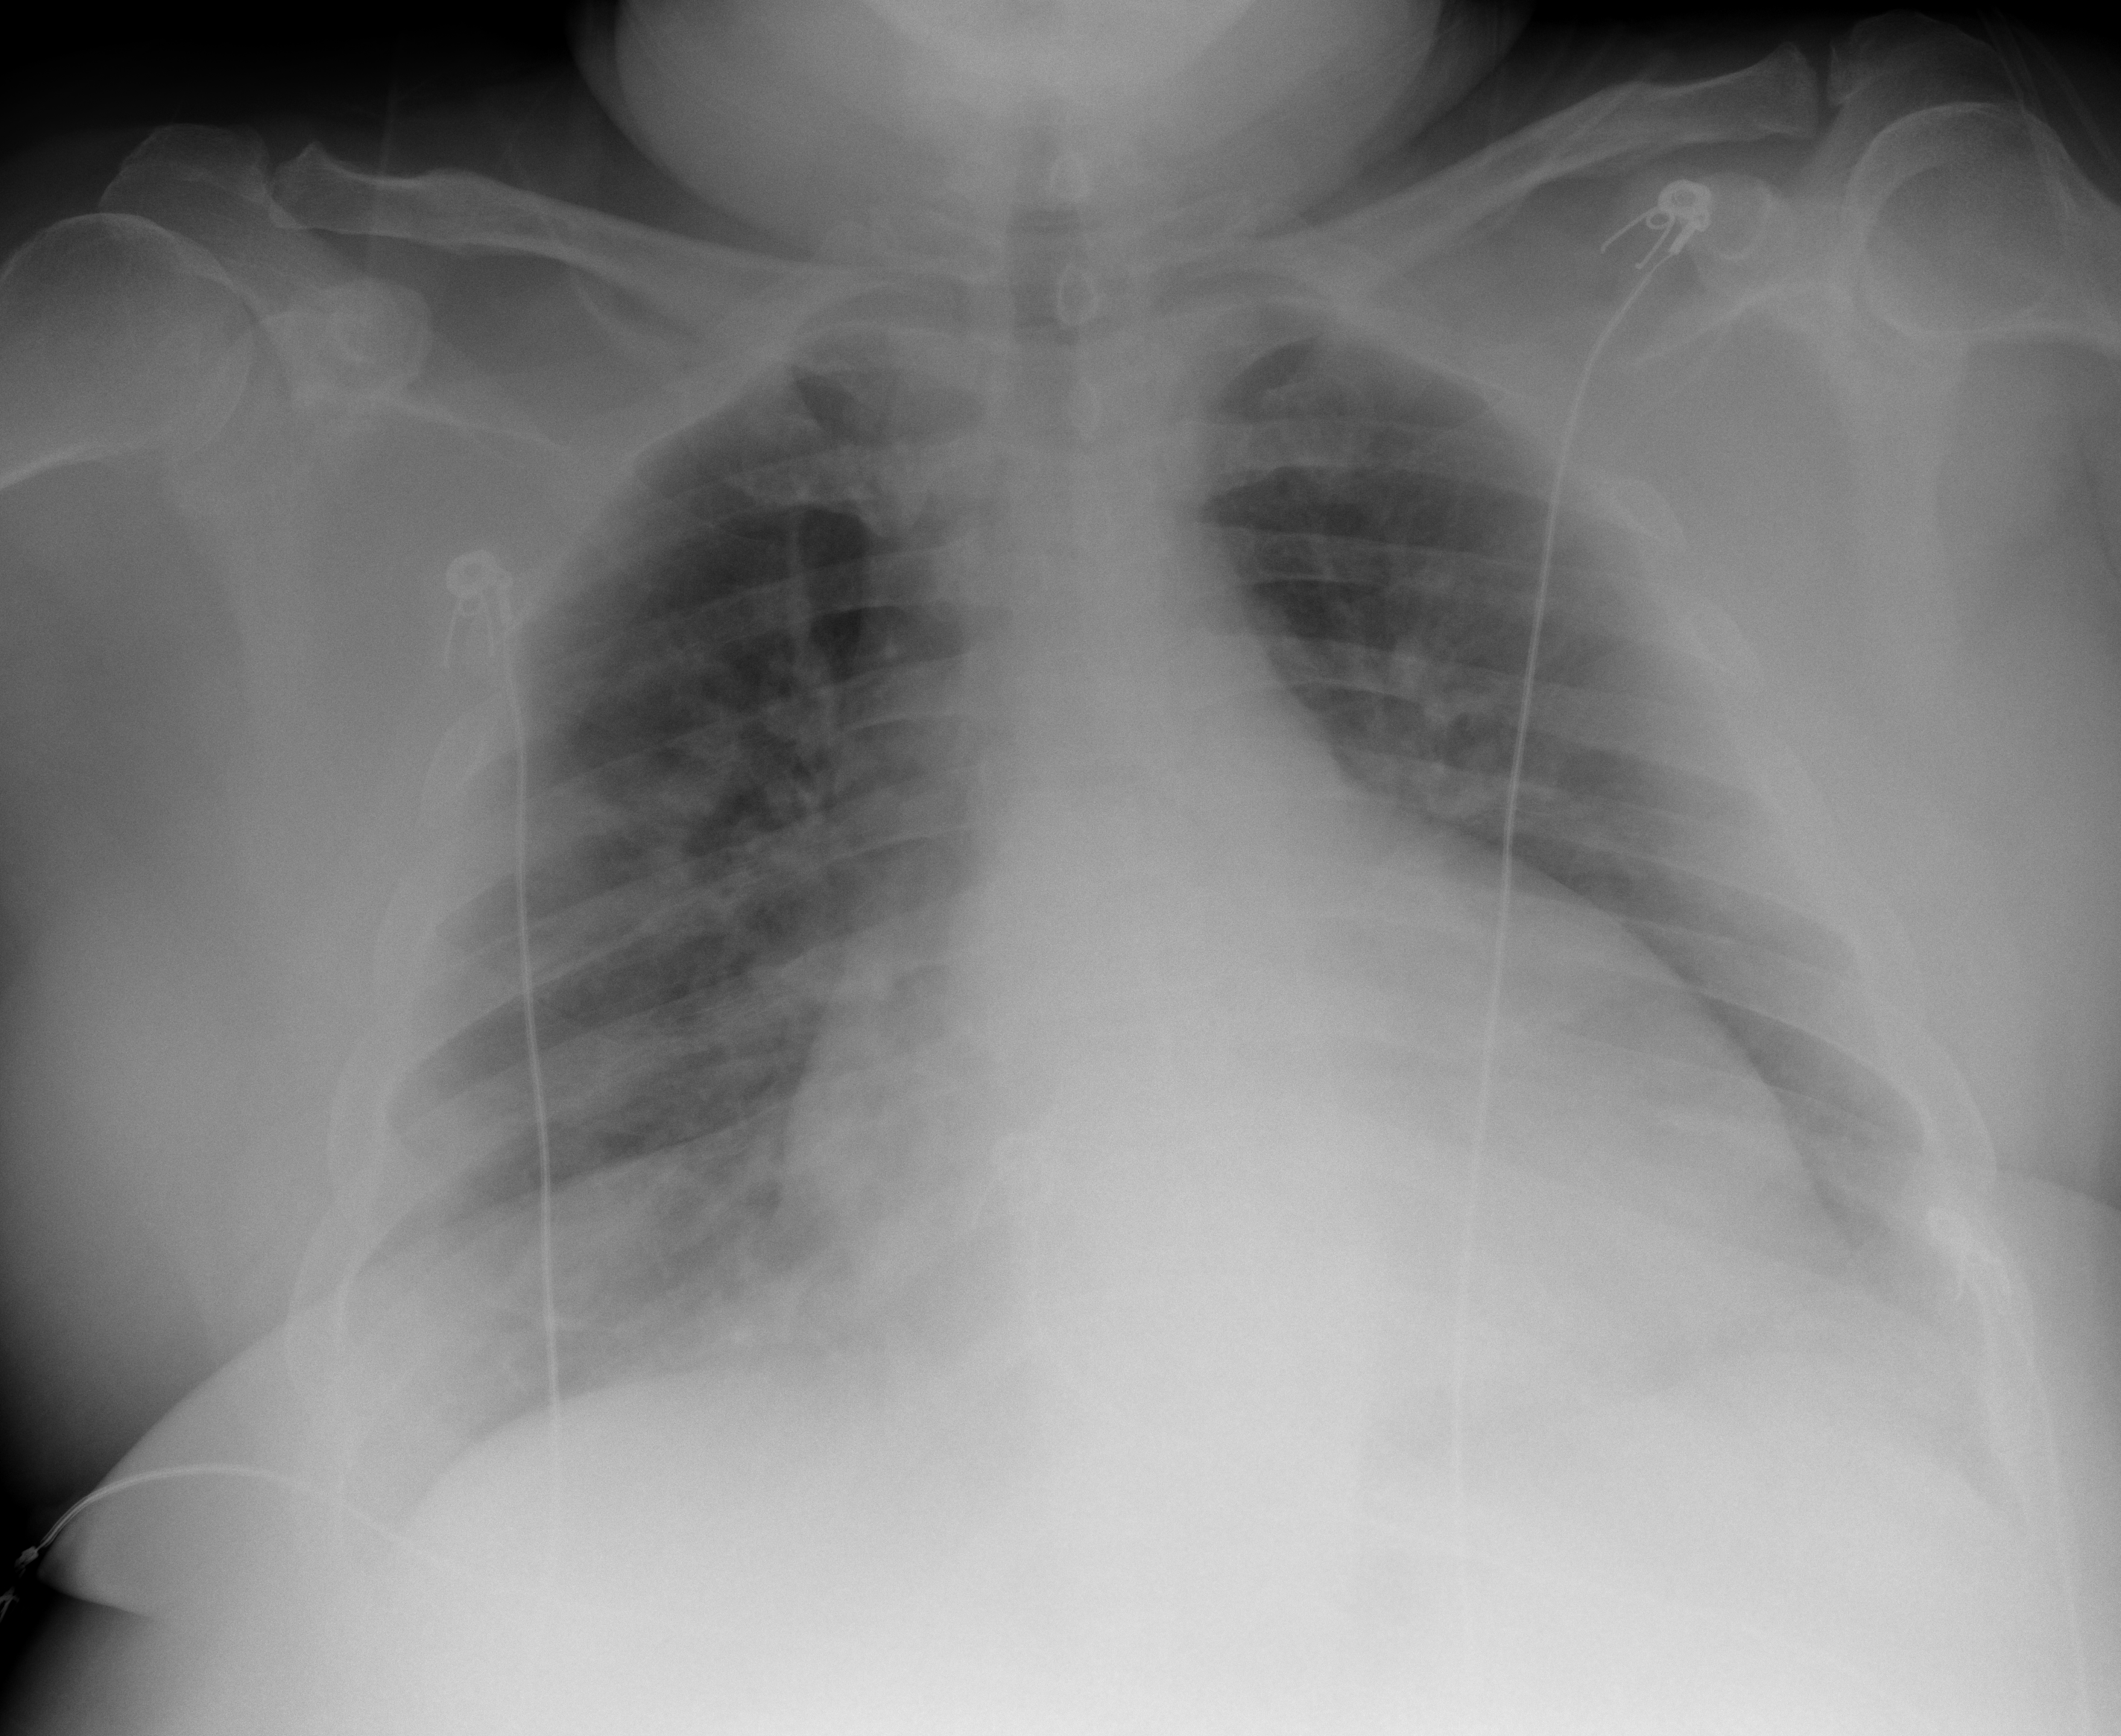
Portable chest radiograph, AP projection. Male patient, age 55 years; imaged 0 days after the COVID-19 diagnosis.
Radiologist's key findings for this exam: subtle hazy opacities noted predominantly within the lung bases.